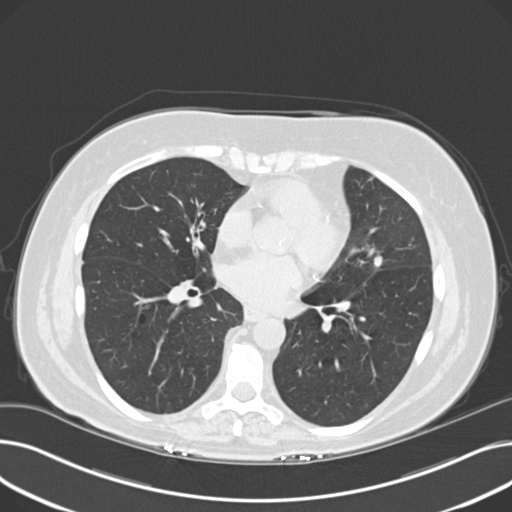
Low-dose screening chest CT, axial slice. Third screening round (two years after baseline). Lung window (W 1500 / L -600 HU). 2 mm slice thickness. 120 kVp. Slice 113 of 203 in the series. Female participant, aged 60 years at enrolment. Current smoker at enrolment.
Expert reader's lesion annotation, bounding box <361,250,399,282> (left, top, right, bottom; pixels). The screening reader recorded 8 non-calcified nodules or masses ≥4 mm on this exam (right upper lobe, lingula, lingula, right middle lobe, right lower lobe, left lower lobe, left lower lobe, left lower lobe); which of them this box marks is not recorded. Later outcome: lung cancer diagnosed 176 days after this screen — non-small cell carcinoma, left upper lobe, poorly differentiated (G3), stage IB (AJCC 6th edition), 7 mm at pathology.